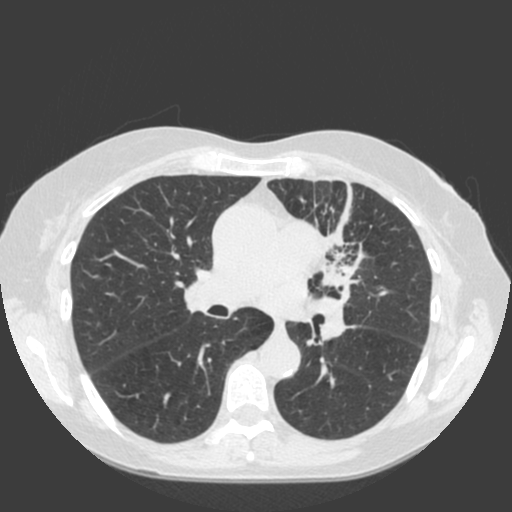
Low-dose screening chest CT, one axial slice; slice 110 of 184 in the series (ordered by position); 120 kVp; lung window (W 1500 / L -600 HU); 2 mm slice thickness; 512 × 512 image matrix, field of view 350 × 350 mm.
Structures marked on this image (outlined manually by an expert reader):
- lesion 1 (tumor, hilum of left lung): bounding box (x1, y1, x2, y2) in pixels: (316, 230, 356, 341)